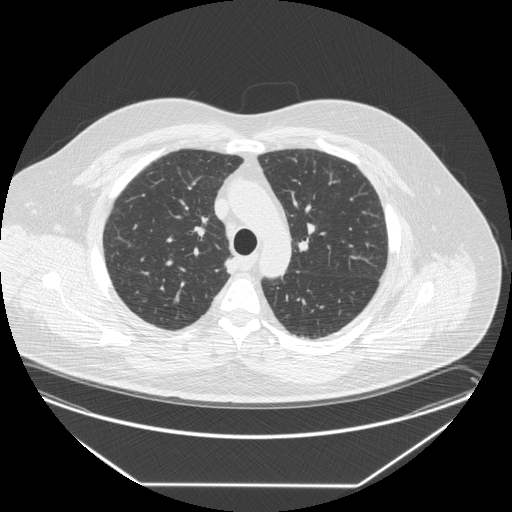
Low-dose screening chest CT, one axial slice. Lung window (W 1500 / L -600 HU). 512 × 512 image matrix, field of view 440 × 440 mm.
Structures marked on this image (outlined manually by an expert reader):
- lesion 1 (tumor, upper lobe of right lung): bounding box (x1, y1, x2, y2) in pixels: (225, 256, 239, 274)